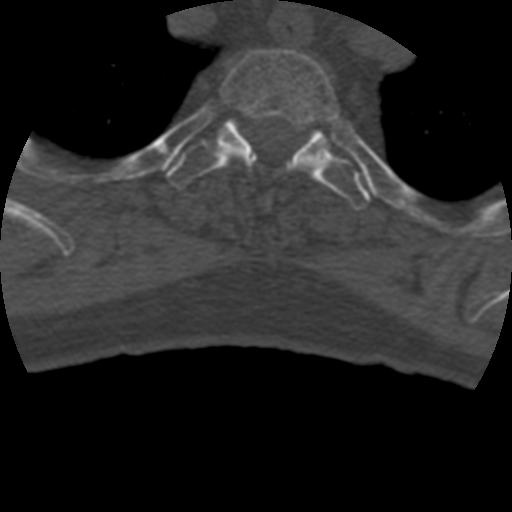
CT including the spine, one axial slice; slice 360 of 399 in the series (ordered by position); reconstruction kernel STANDARD; 120 kVp; bone window (W 1800 / L 400 HU); 512 × 512 image matrix, field of view 160 × 160 mm. Patient age 69 years. Case-level facts recorded for this patient, not image findings: primary cancer: prostate.
Structures marked on this image (semi-automatic segmentation, software-assisted and operator-edited):
- T2 vertebra: bounding box (x1, y1, x2, y2) in pixels: (219, 50, 339, 177)
- T3 vertebra: (167, 118, 371, 210)